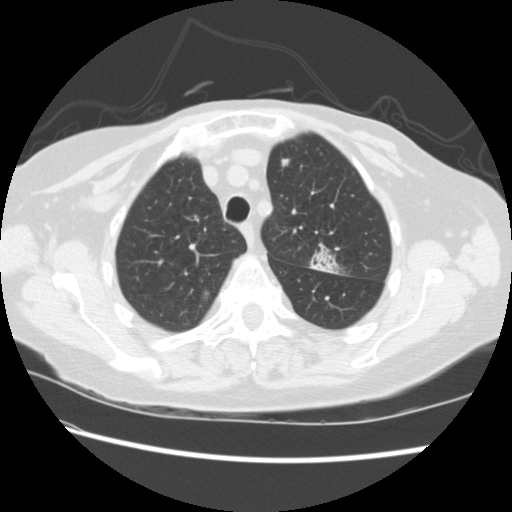
Chest CT (low-dose screening protocol), one axial image. Baseline screening round. Lung window (W 1500 / L -600 HU). 2.5 mm slice thickness. Standard (soft-tissue) reconstruction kernel (STANDARD). Female participant, aged 74 years at enrolment. Former smoker at enrolment.
Expert reader's lesion annotation, bounding box (x1, y1, x2, y2) in pixels: (297, 238, 347, 281). The screening reader recorded 2 non-calcified nodules or masses ≥4 mm on this exam; which of them this box marks is not recorded. Official screen result: positive, change unspecified: nodule(s) >= 4 mm or enlarging nodule(s), mass(es), or other non-specific abnormalities suspicious for lung cancer.